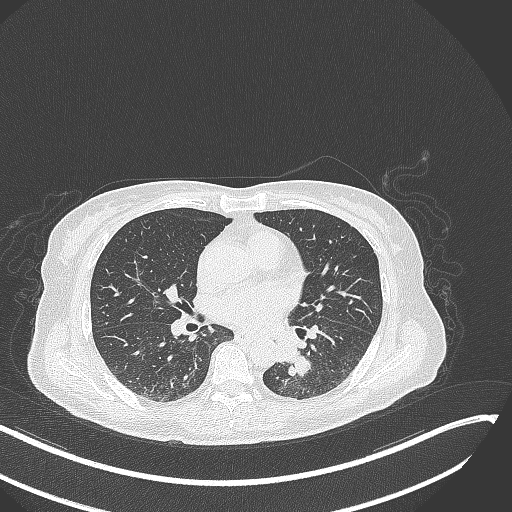
Chest CT, one axial slice. Position 131 of 342 along the scan axis. Lung window (W 1500 / L -600 HU). 1 mm slice thickness. 512 × 512 image matrix, field of view 400 × 400 mm. Patient: female, 64 years. From the clinical record (not read from this slice): clinical TNM (as recorded): T3 N1 M1.
Structures marked on this image (rectangle marked by the reading radiologist):
- lung tumour (recorded histology: small cell carcinoma): bounding box (x1, y1, x2, y2) in pixels: (269, 335, 312, 380)